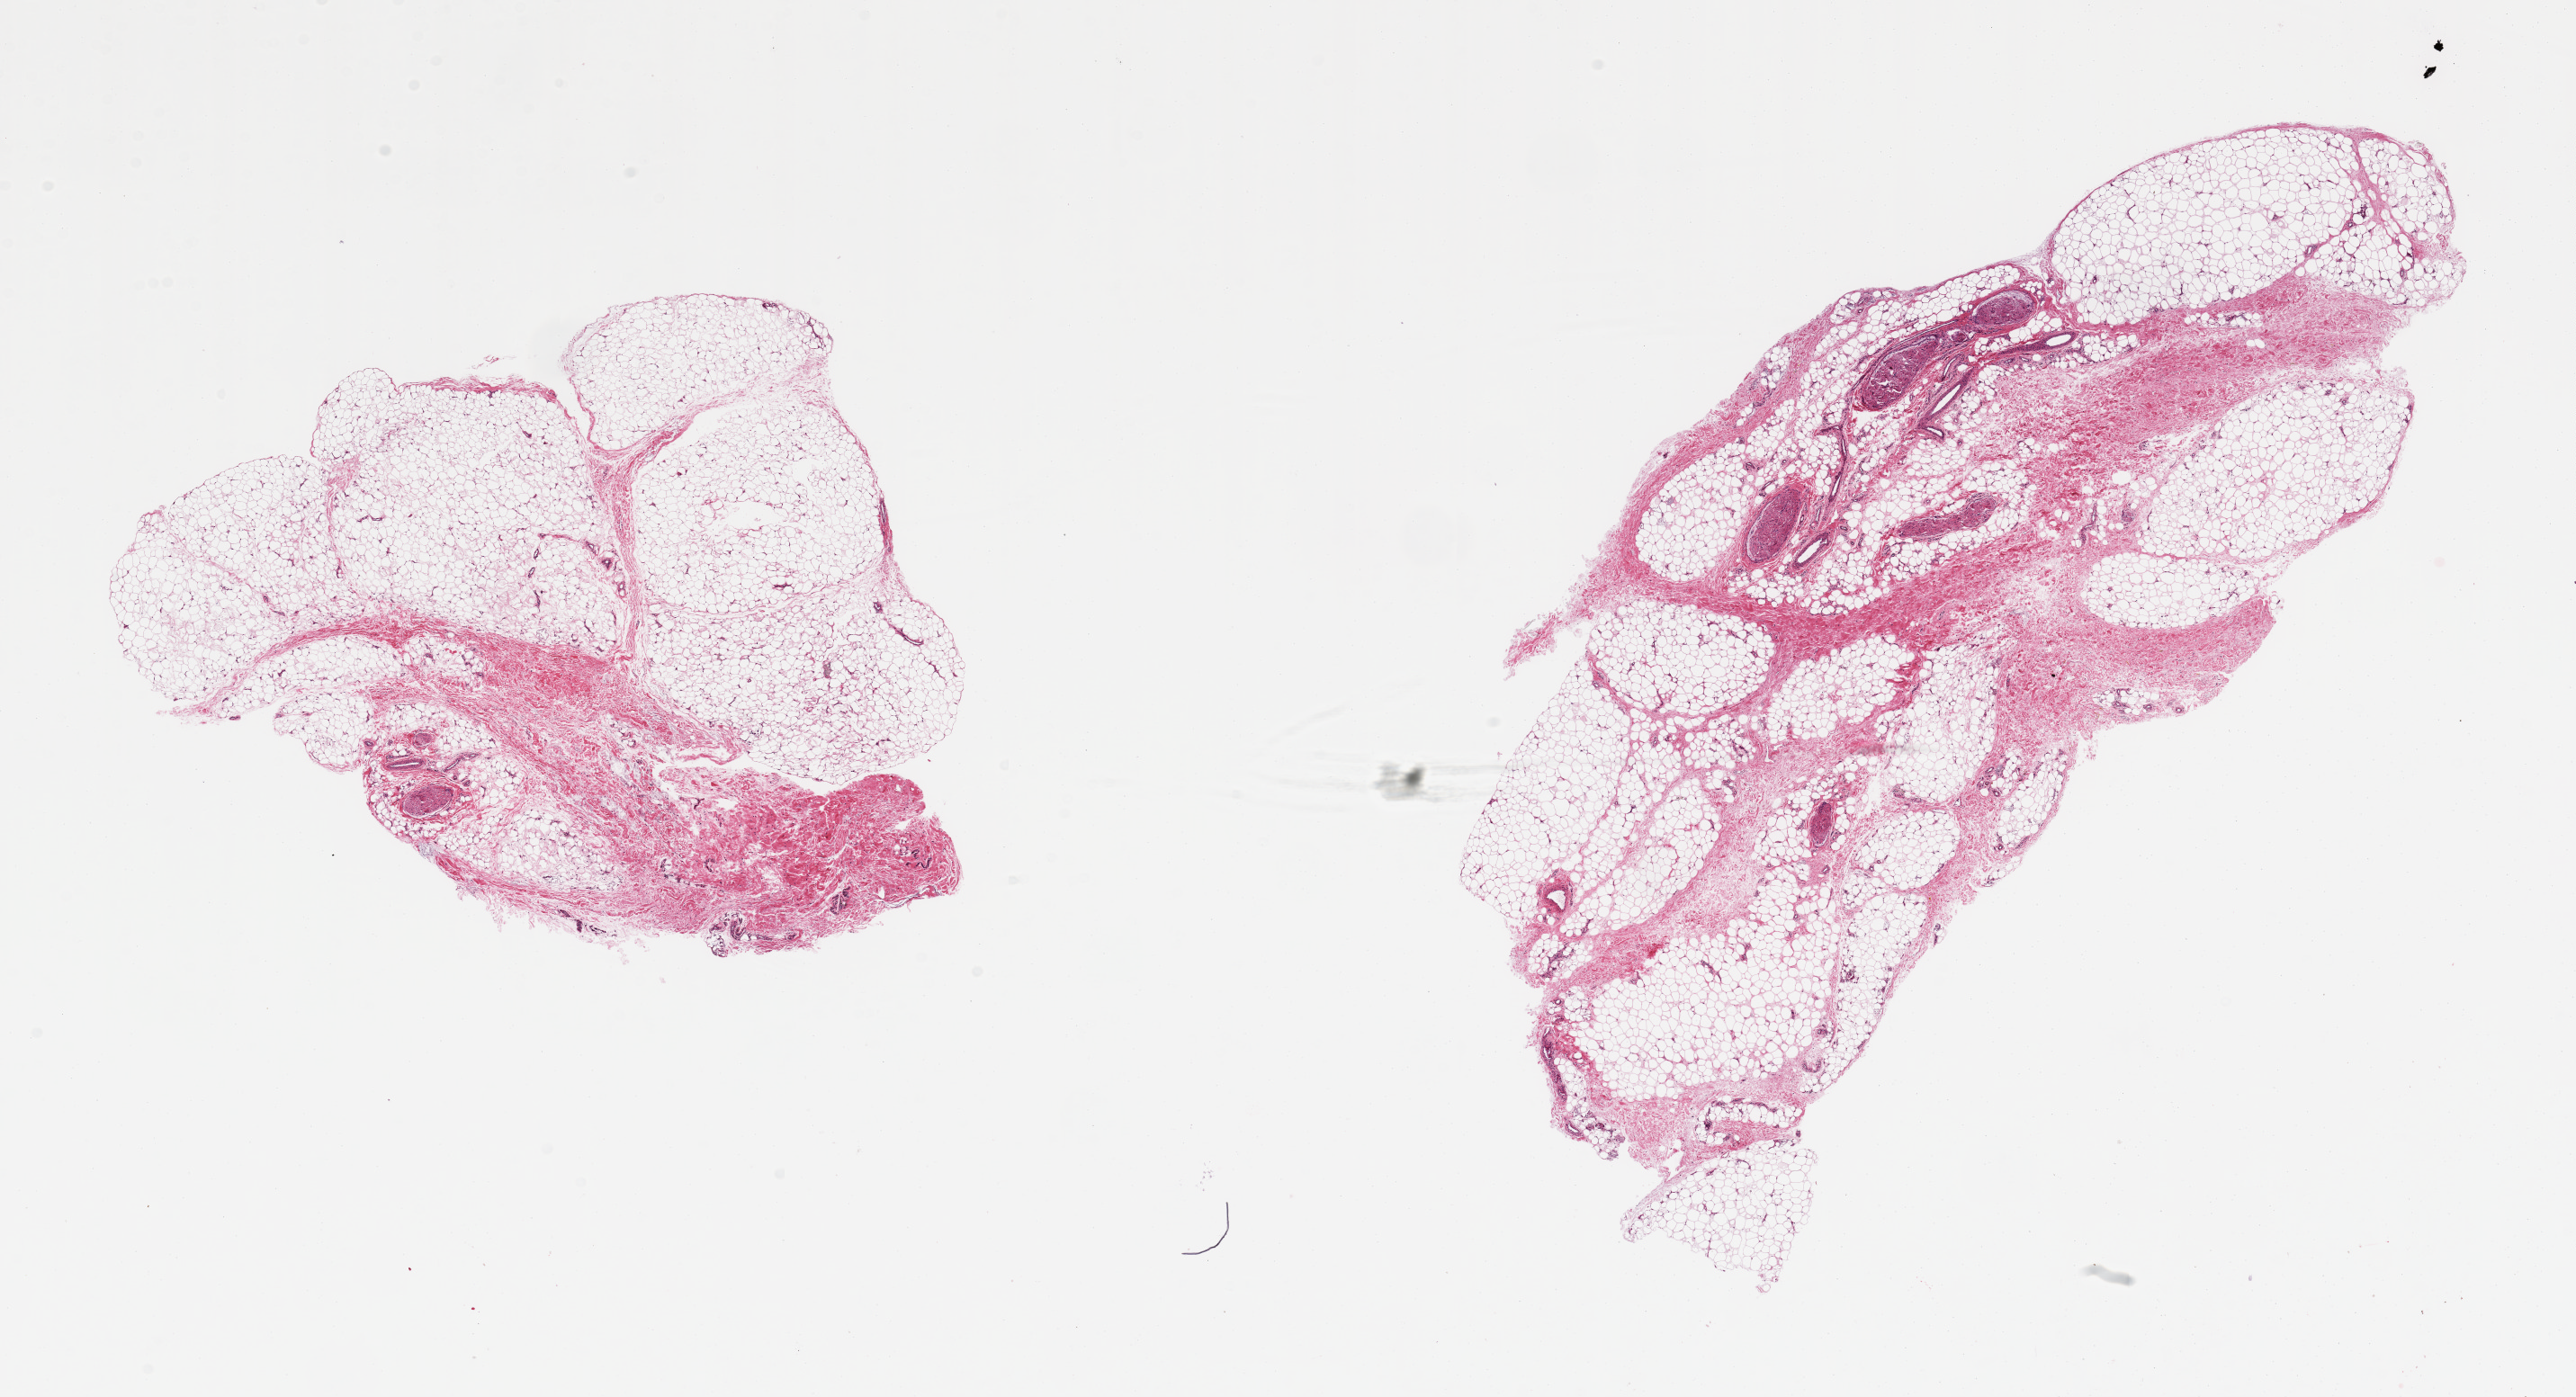
Haematoxylin and eosin whole-slide image, brightfield, shown as a low-resolution overview of the whole scanned area (about 22.6 x 12.3 mm), PAXgene-fixed, paraffin-embedded tissue, target tissue: adipose tissue, donor tissue sample. Donor sex: male.
Pathologist's review note for this sample: 2 pieces; 20% fibrous content; 5% nerve.